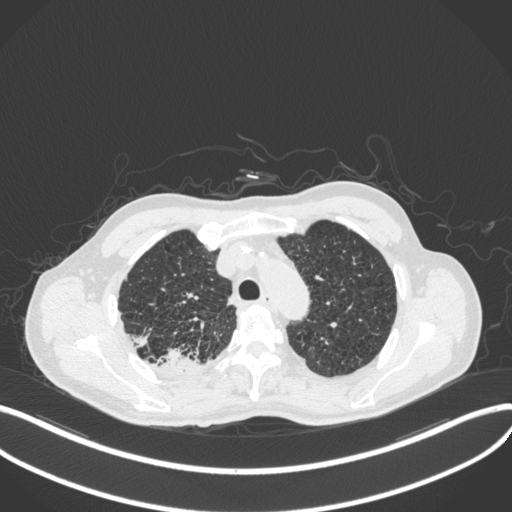
Chest CT, one axial slice; slice 348 of 423 in the series (ordered by position); reconstruction kernel B31f; lung window (W 1500 / L -600 HU); 512 × 512 image matrix, field of view 400 × 400 mm. Patient: male, 79 years. Case-level facts recorded for this patient, not image findings: clinical TNM (as recorded): T3 N0 M0.
Structures marked on this image (bounding box drawn by a radiologist):
- lung tumour (recorded histology: adenocarcinoma): bounding box [x1, y1, x2, y2] px = [156, 346, 199, 373]